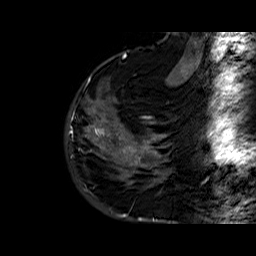
Breast MRI (dynamic contrast-enhanced), one sagittal slice. Position 13 of 60 along the scan axis. Dynamic contrast-enhanced series, time point 2 of 6 at this slice position (early post-contrast). 1.5 T. TE 6.4 ms, TR 32.8 ms. 4 mm slice thickness. 256 × 256 image matrix, field of view 200 × 200 mm. Female patient. Case-level facts recorded for this patient, not image findings: setting: breast cancer imaged before/during neoadjuvant chemotherapy; receptor status: HR-positive, HER2-negative.
Structures marked on this image (semi-automatically segmented with operator editing):
- analysis volume of interest (the breast-tissue region the enhancement analysis was run in; not a lesion): bounding box <86,77,163,177> (left, top, right, bottom; pixels)
- tumour enhancement mask (voxels above the 100 % enhancement threshold inside the analysis volume of interest): <89,77,153,163>